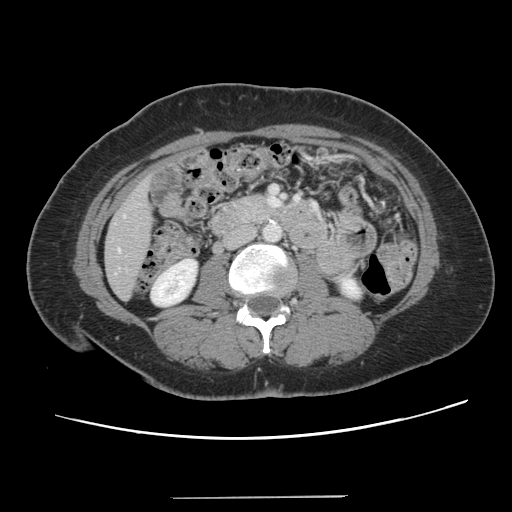
Contrast-enhanced abdominal CT, one axial slice; slice 34 of 141 in the series (ordered by position); intravenous contrast given; soft-tissue window (W 400 / L 40 HU); 2.5 mm slice thickness; 512 × 512 image matrix, field of view 366 × 366 mm. Female patient, age 53 years. Case-level facts recorded for this patient, not image findings: diagnosis: colorectal cancer liver metastases, imaged before liver resection; multiple liver metastases: no; largest metastasis: 14.5 cm; disease in both lobes: yes.
Outlined on this slice (expert manual segmentation):
- liver: box from (x=106, y=181) to (x=153, y=299) px
- planned liver remnant (the part of the liver to remain after resection): (x=105, y=210)–(x=153, y=298)